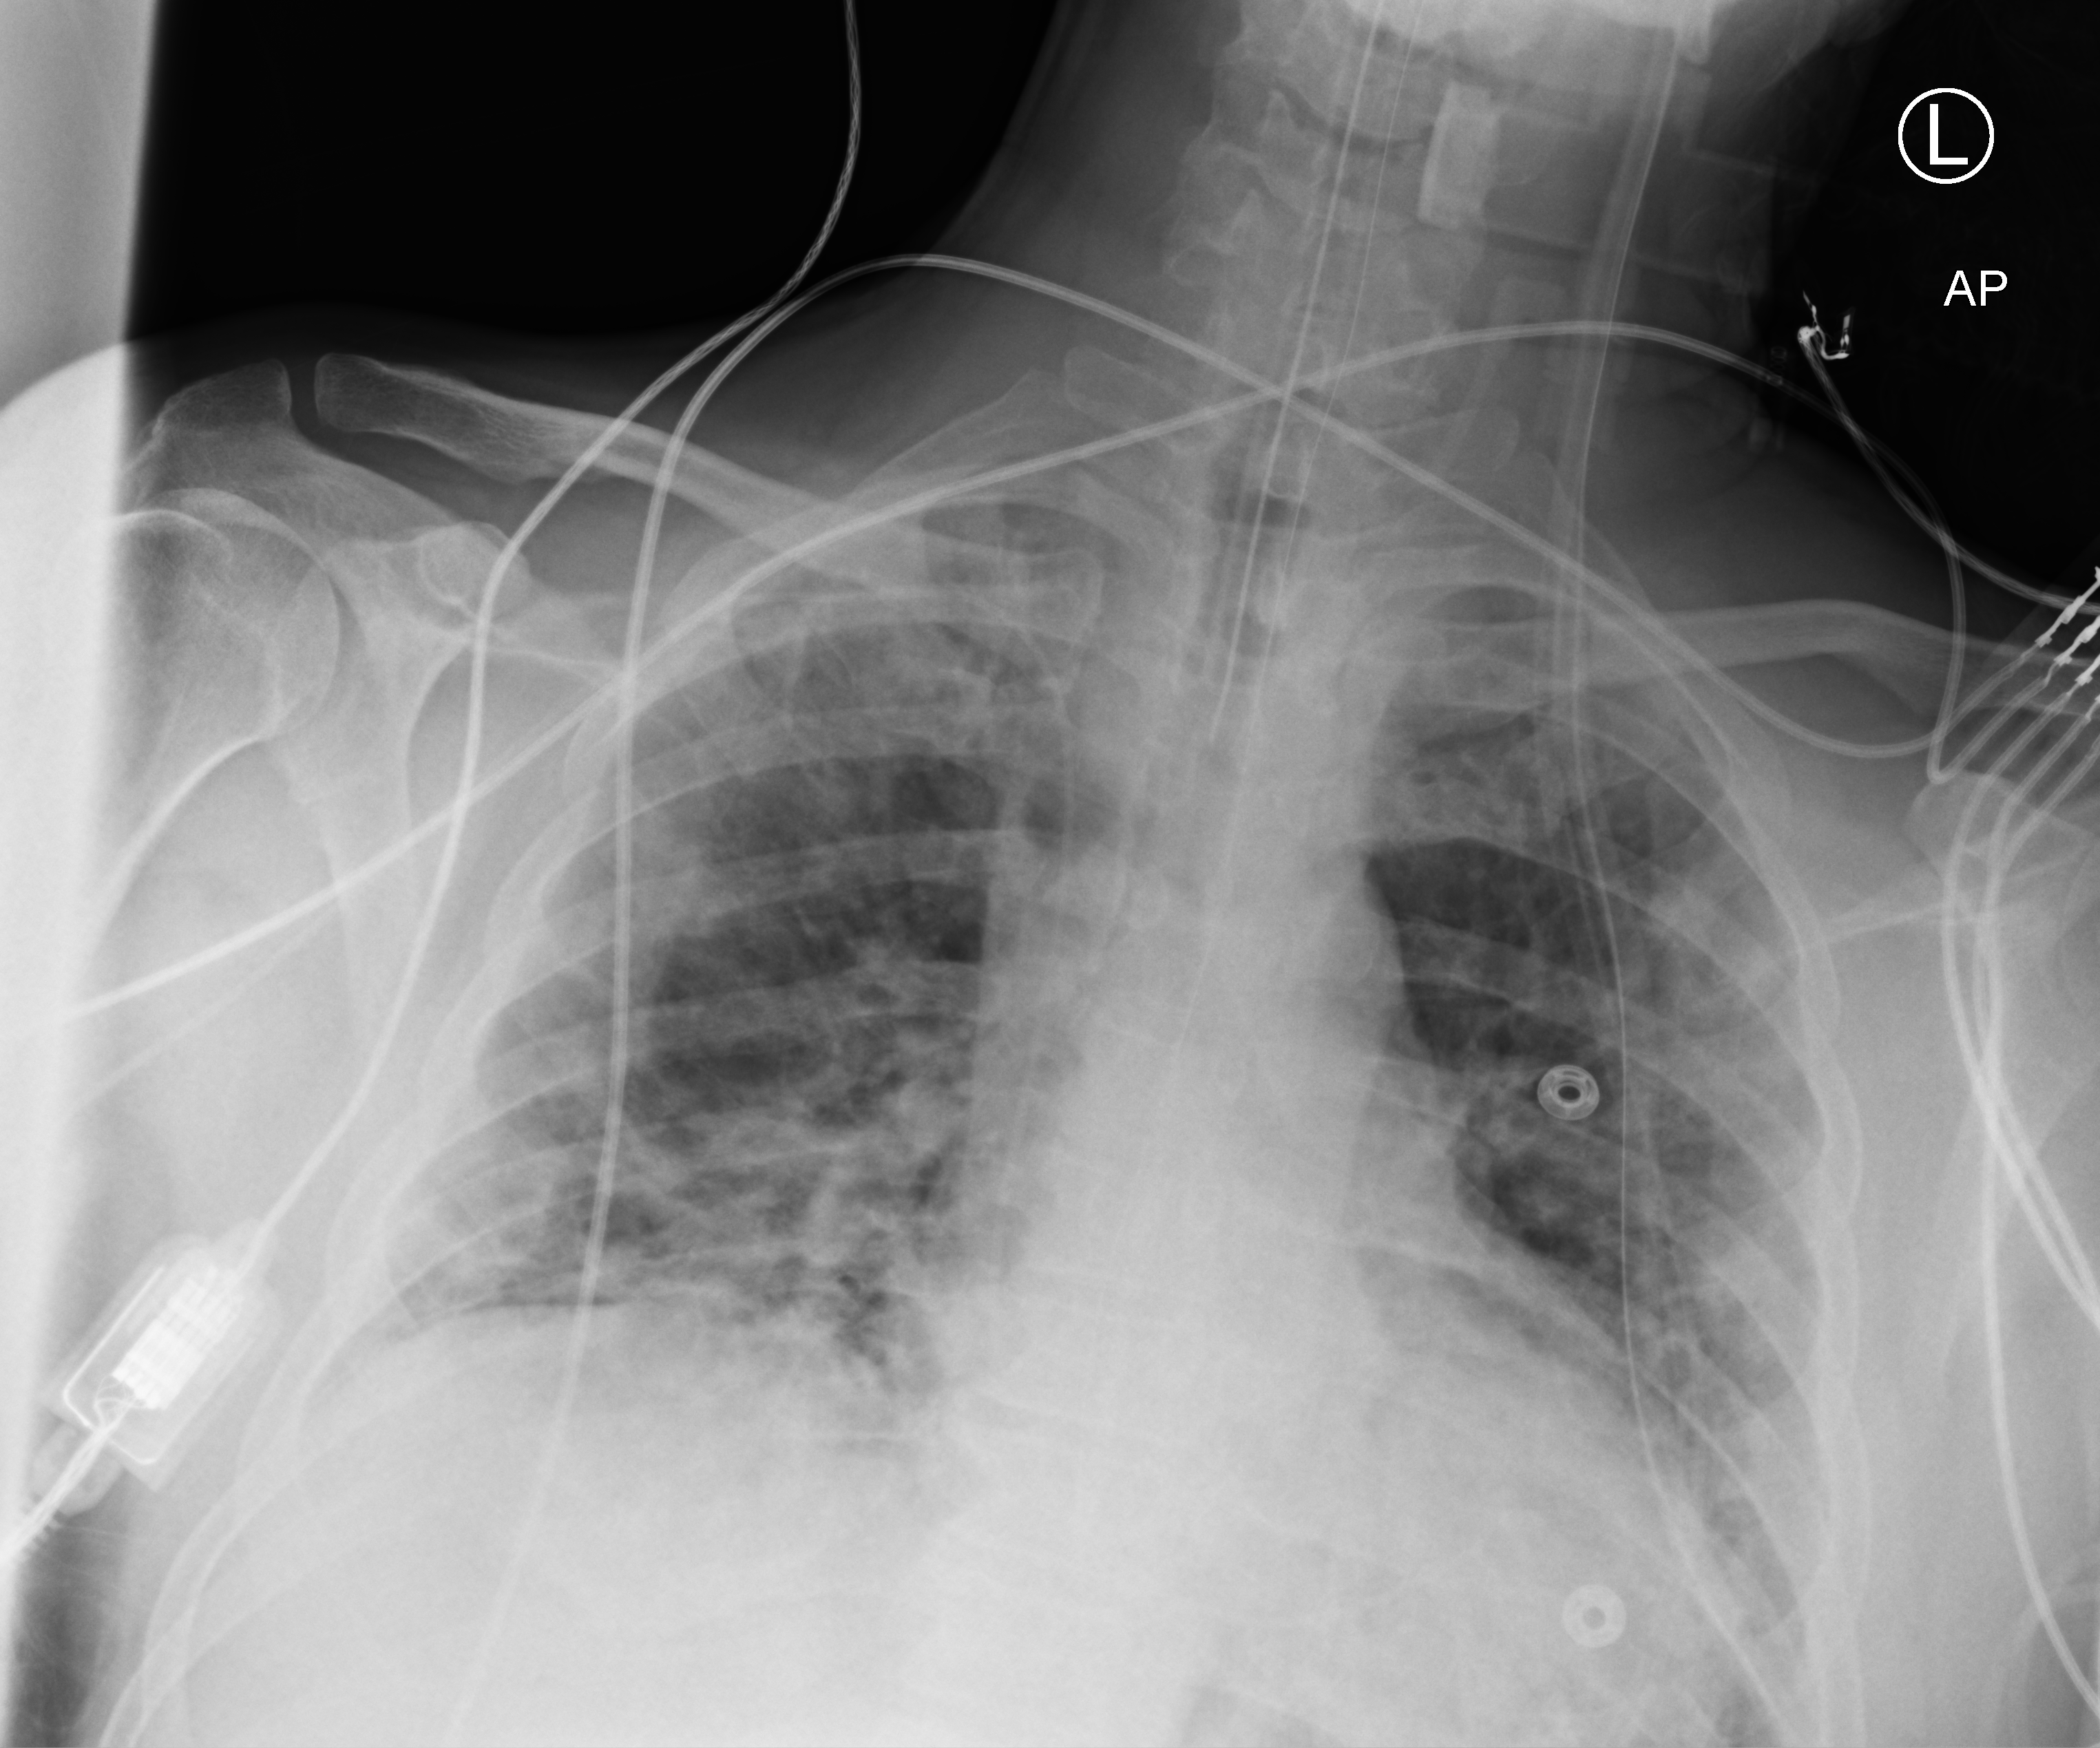
Chest X-ray (portable); anteroposterior (AP) projection. Male patient hospitalised with COVID-19, age 18–59 years.
Hospital-stay facts (about this admission, not read from this image; timing relative to this image not recorded): length of hospital stay: 32 days; admitted to intensive care during this hospital stay: no; mechanically ventilated during this hospital stay: yes.